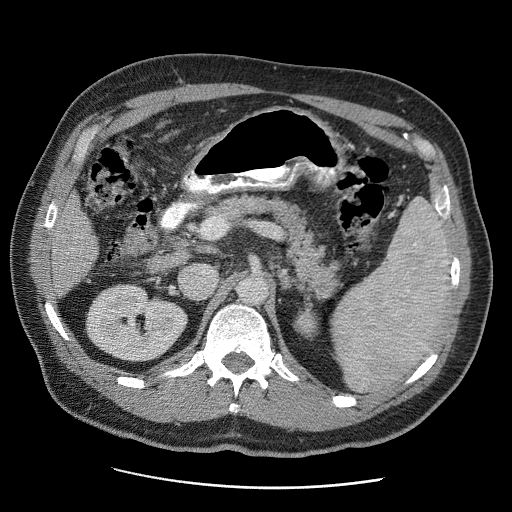
Contrast-enhanced abdominal CT (liver protocol), one axial slice; position 16 of 81 along the scan axis; reconstruction kernel STANDARD; 120 kVp; soft-tissue window (W 400 / L 40 HU); 2.5 mm slice thickness; 512 × 512 image matrix, field of view 380 × 380 mm. Case-level facts recorded for this patient, not image findings: diagnosis: hepatocellular carcinoma (patient treated with transarterial chemoembolisation; whether this scan precedes or follows treatment is not stated here); TNM stage (as recorded): Stage-IIIA; Child-Pugh class: A; tumour differentiation: moderately differentiated; tumour nodularity: multinodular.
Structures marked on this image (semi-automatically segmented with operator editing):
- liver parenchyma outside the tumour (the mass and vessels are separate outlines, so this box may not span the whole liver): bounding box [x1, y1, x2, y2] px = [52, 194, 98, 296]
- liver vessels: [52, 213, 57, 223]